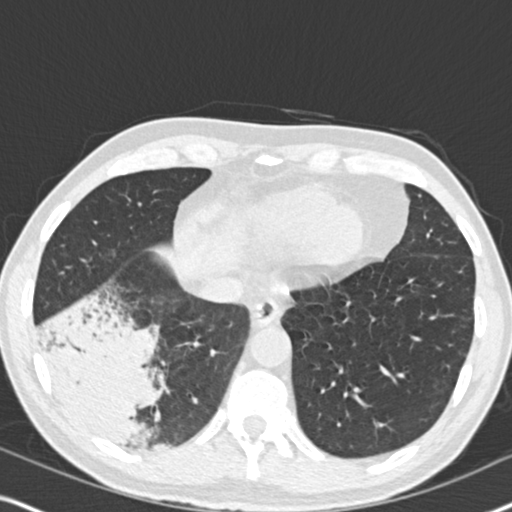
Low-dose screening chest CT, axial slice; second annual screen; lung window (W 1500 / L -600 HU); 2 mm slice thickness; slice 122 of 182 in the series; 512 × 512 image matrix. Male participant, aged 61 years at enrolment. Current smoker at enrolment.
• Lesion marked by an expert reader, bounding box (x1, y1, x2, y2) in pixels: (31, 298, 183, 458).
• Screening reader's record for this exam (one nodule recorded; not confirmed to be the boxed lesion): non-calcified nodule or mass ≥4 mm, right lower lobe, 90 × 80 mm, soft tissue attenuation, pre-existing on the prior screen: yes; interval growth: yes.
• Official screen result: positive, other.
• Lung cancer was diagnosed 20 days after this screen: bronchiolo-alveolar adenocarcinoma, NOS, right lower lobe, moderately differentiated (G2), stage IIIB (AJCC 6th edition), 90 mm at pathology.